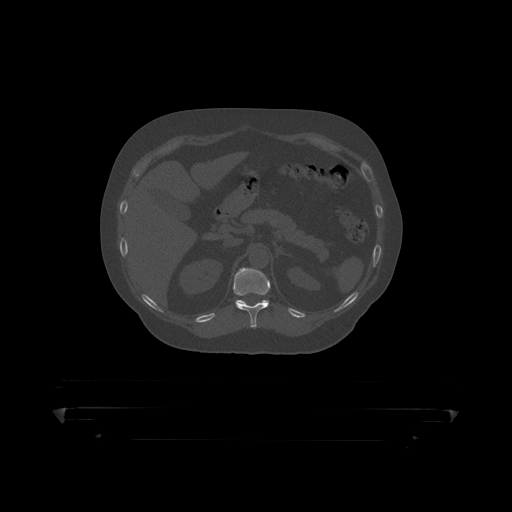
CT including the spine, one axial slice. Position 189 of 390 along the scan axis. Reconstruction kernel STANDARD. 120 kVp. Bone window (W 1800 / L 400 HU). 512 × 512 image matrix. Patient: male, 60 years. Case-level facts recorded for this patient, not image findings: primary cancer: prostate.
Annotated regions visible in this slice (semi-automatically segmented with operator editing):
- T11 vertebra: box from (x=233, y=268) to (x=291, y=319) px
- T12 vertebra: (x=236, y=300)–(x=269, y=304)